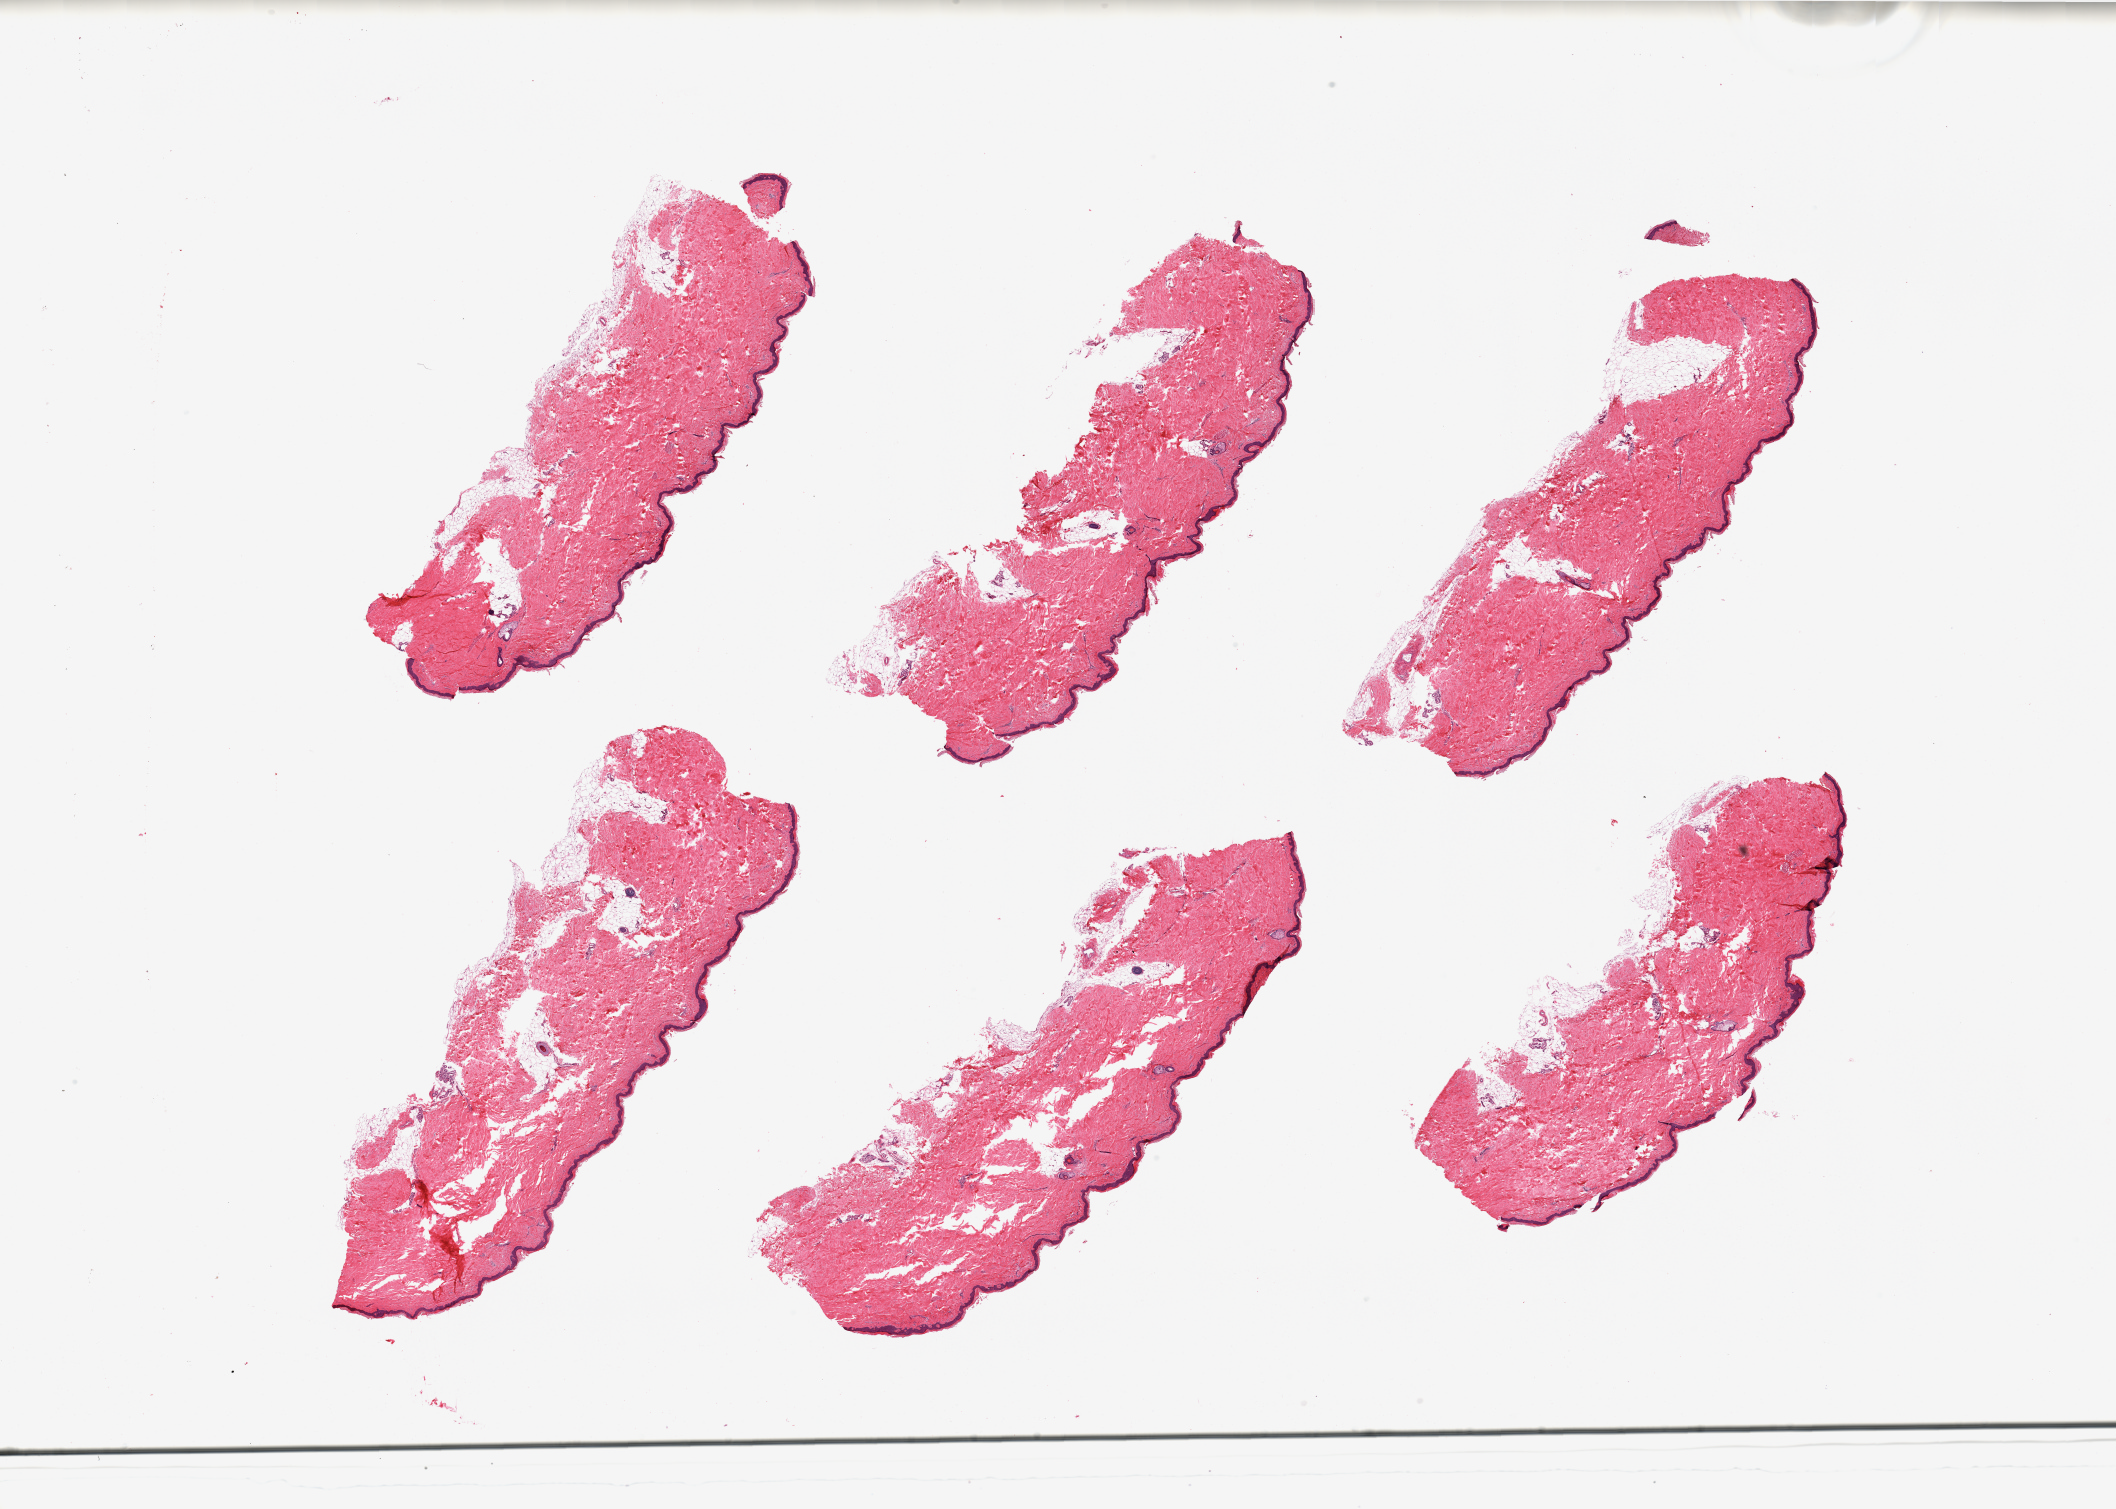
Digitized hematoxylin and eosin (H&E)-stained section, low-resolution overview of the scanned area, about 33.5 x 23.9 mm, PAXgene-fixed, paraffin-embedded tissue, target tissue: skin of lower leg, tissue donor sample. Female donor.
• pathologist's review note for this sample: 6 pieces, trace dermal fat, ~1-2mm nubbins; squamous epithelium is ~50 microns